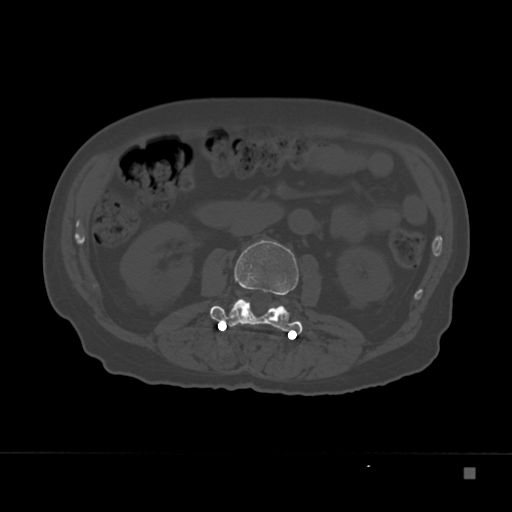
CT including the spine, one axial slice. Slice 85 of 332 in the series (ordered by position). 120 kVp. Bone window (W 1800 / L 400 HU). 1.5 mm slice thickness. 512 × 512 image matrix. Male patient, age 72 years. From the clinical record (not read from this slice): primary cancer: skeletal.
Structures marked on this image (semi-automatically segmented with operator editing):
- L2 vertebra: box from (x=211, y=240) to (x=303, y=335) px
- L3 vertebra: (x=227, y=298)–(x=299, y=332)